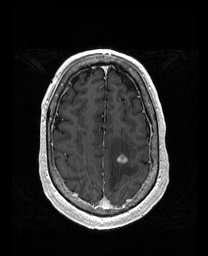
Brain MRI from a brain-tumour surgery series, one axial slice; position 138 of 192 along the scan axis; T1-weighted post-contrast; 1 mm slice thickness; 208 × 256 image matrix, field of view 211 × 260 mm. From the clinical record (not read from this slice): histopathology: Metastatic Carcinoma from Lung Adenocarcinoma.
Outlined on this slice (manually delineated by an expert):
- tumour: bounding box [x1, y1, x2, y2] px = [117, 156, 127, 163]